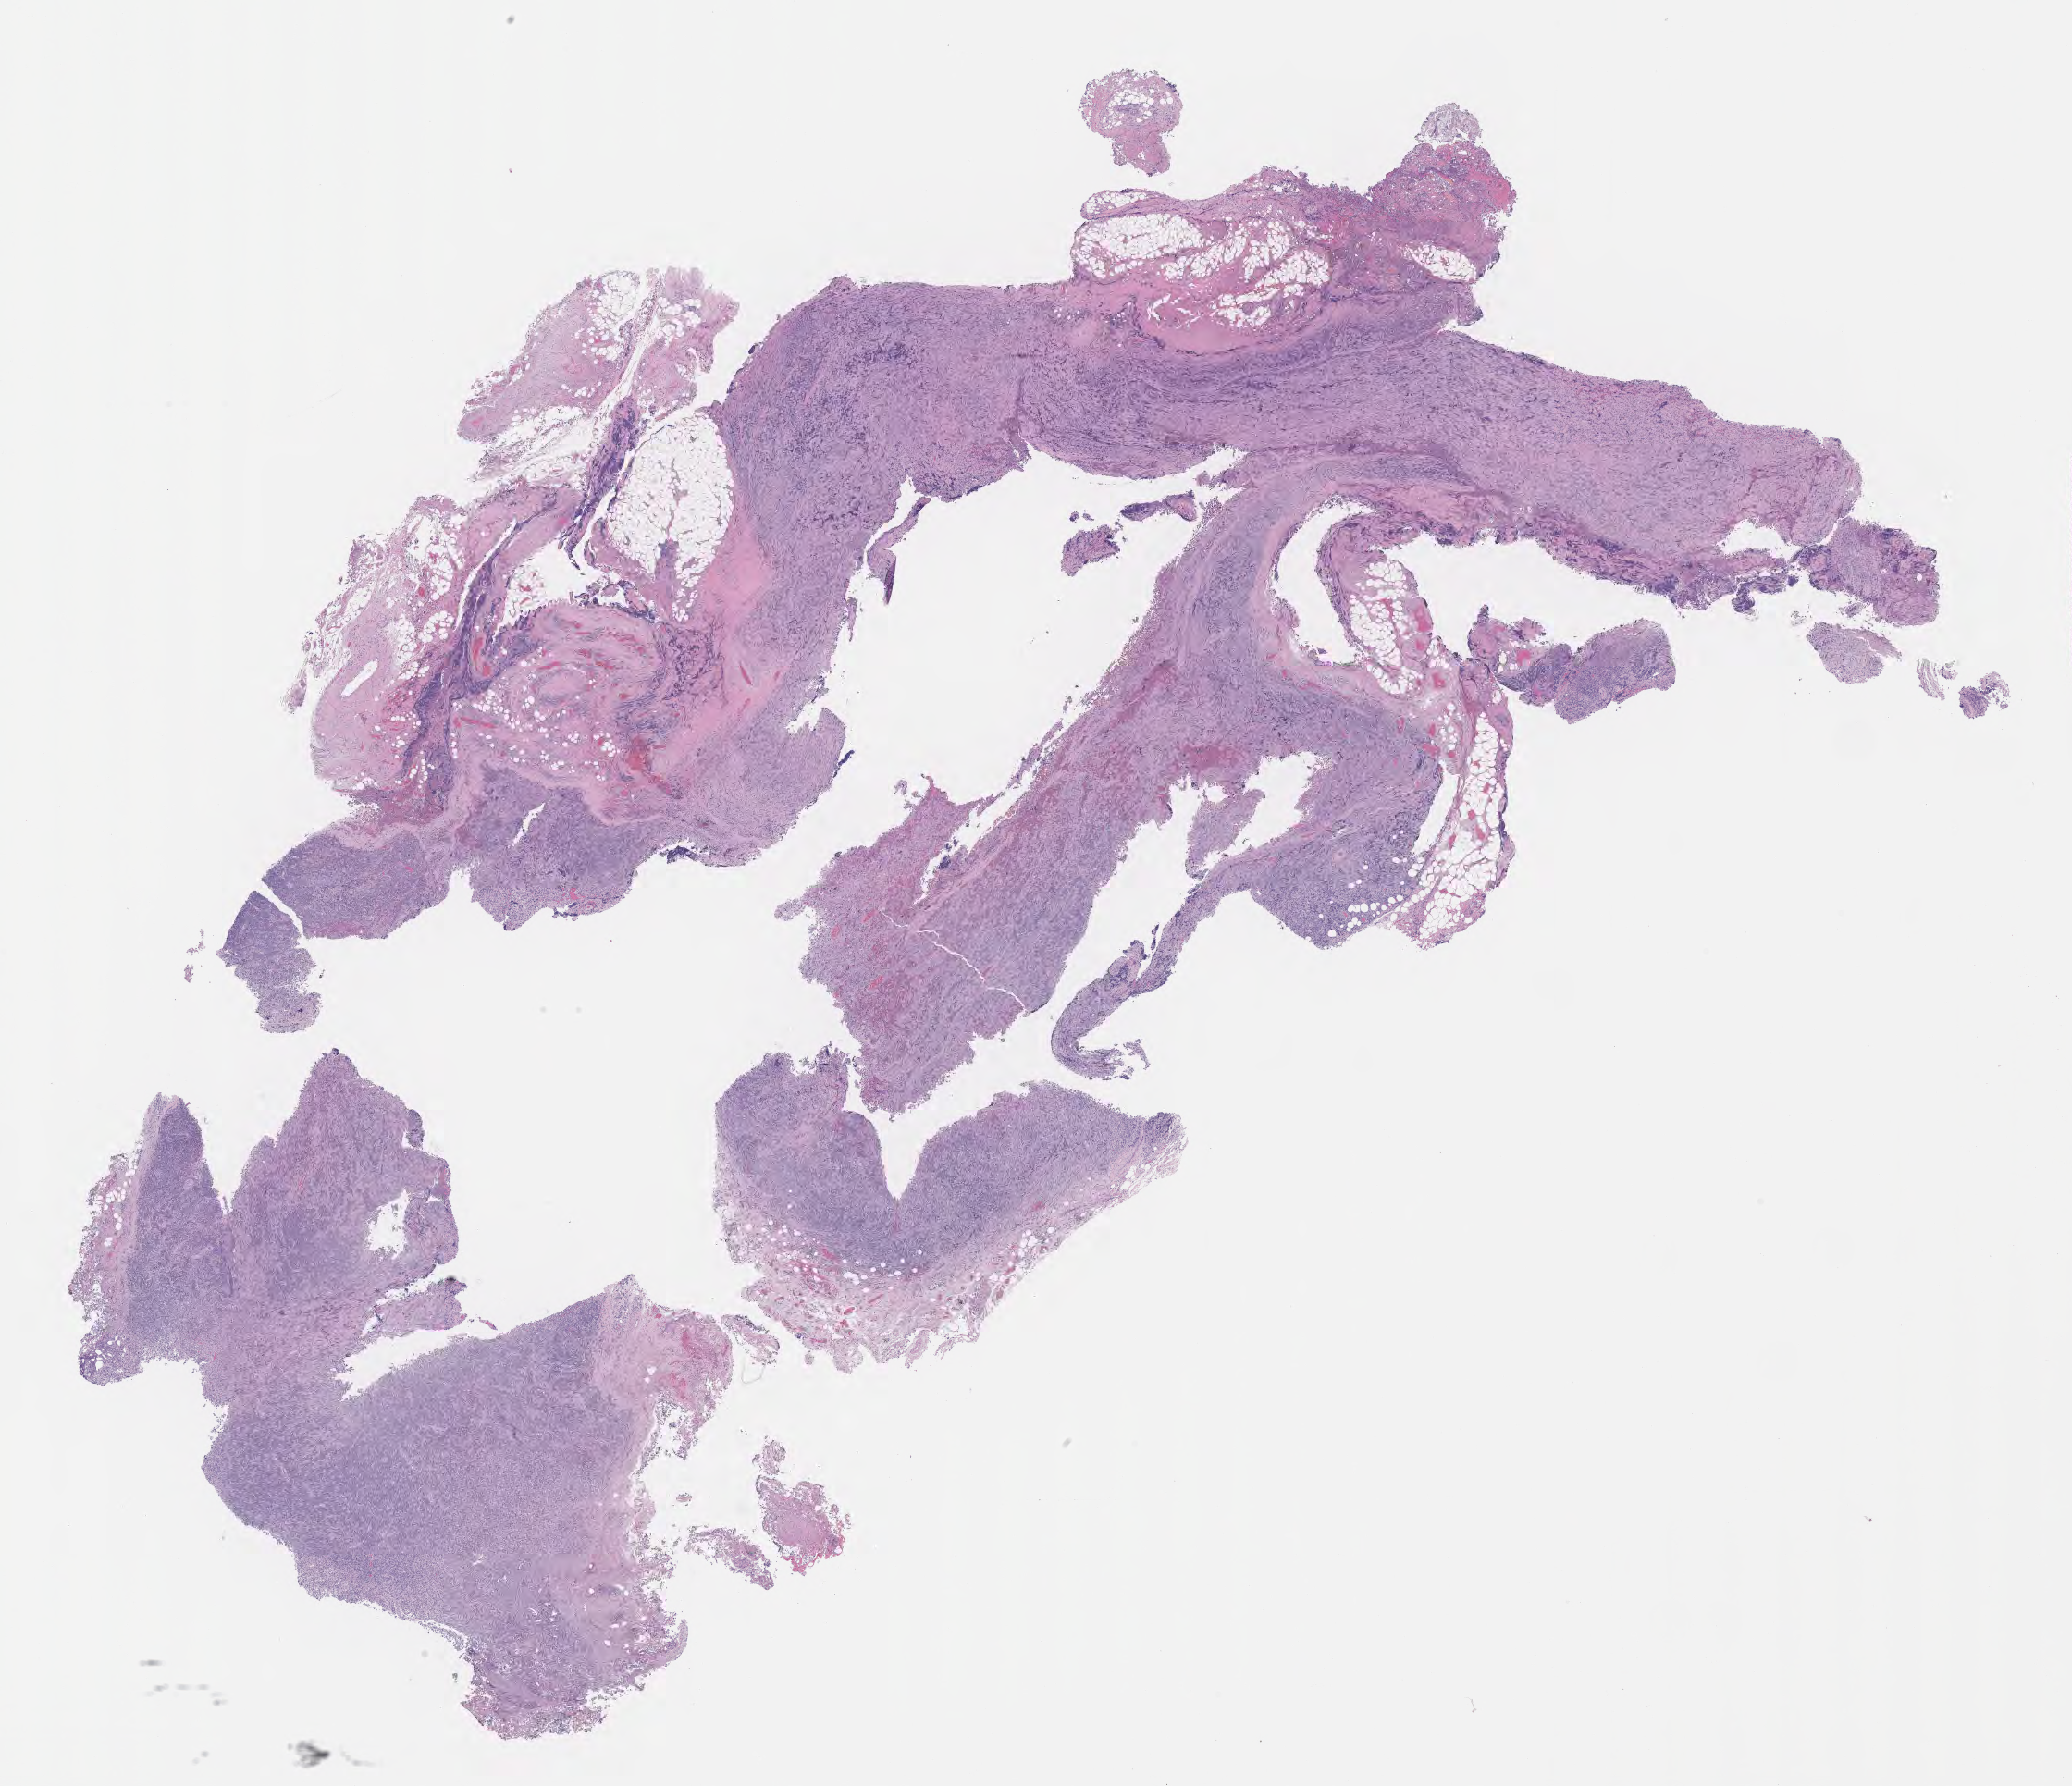
Whole-slide image, H&E stain, a low-resolution overview of the entire scanned area, about 18.1 x 15.6 mm. Tumor tissue. Male patient, 44 years old.
* histologic diagnosis: Burkitt lymphoma, NOS